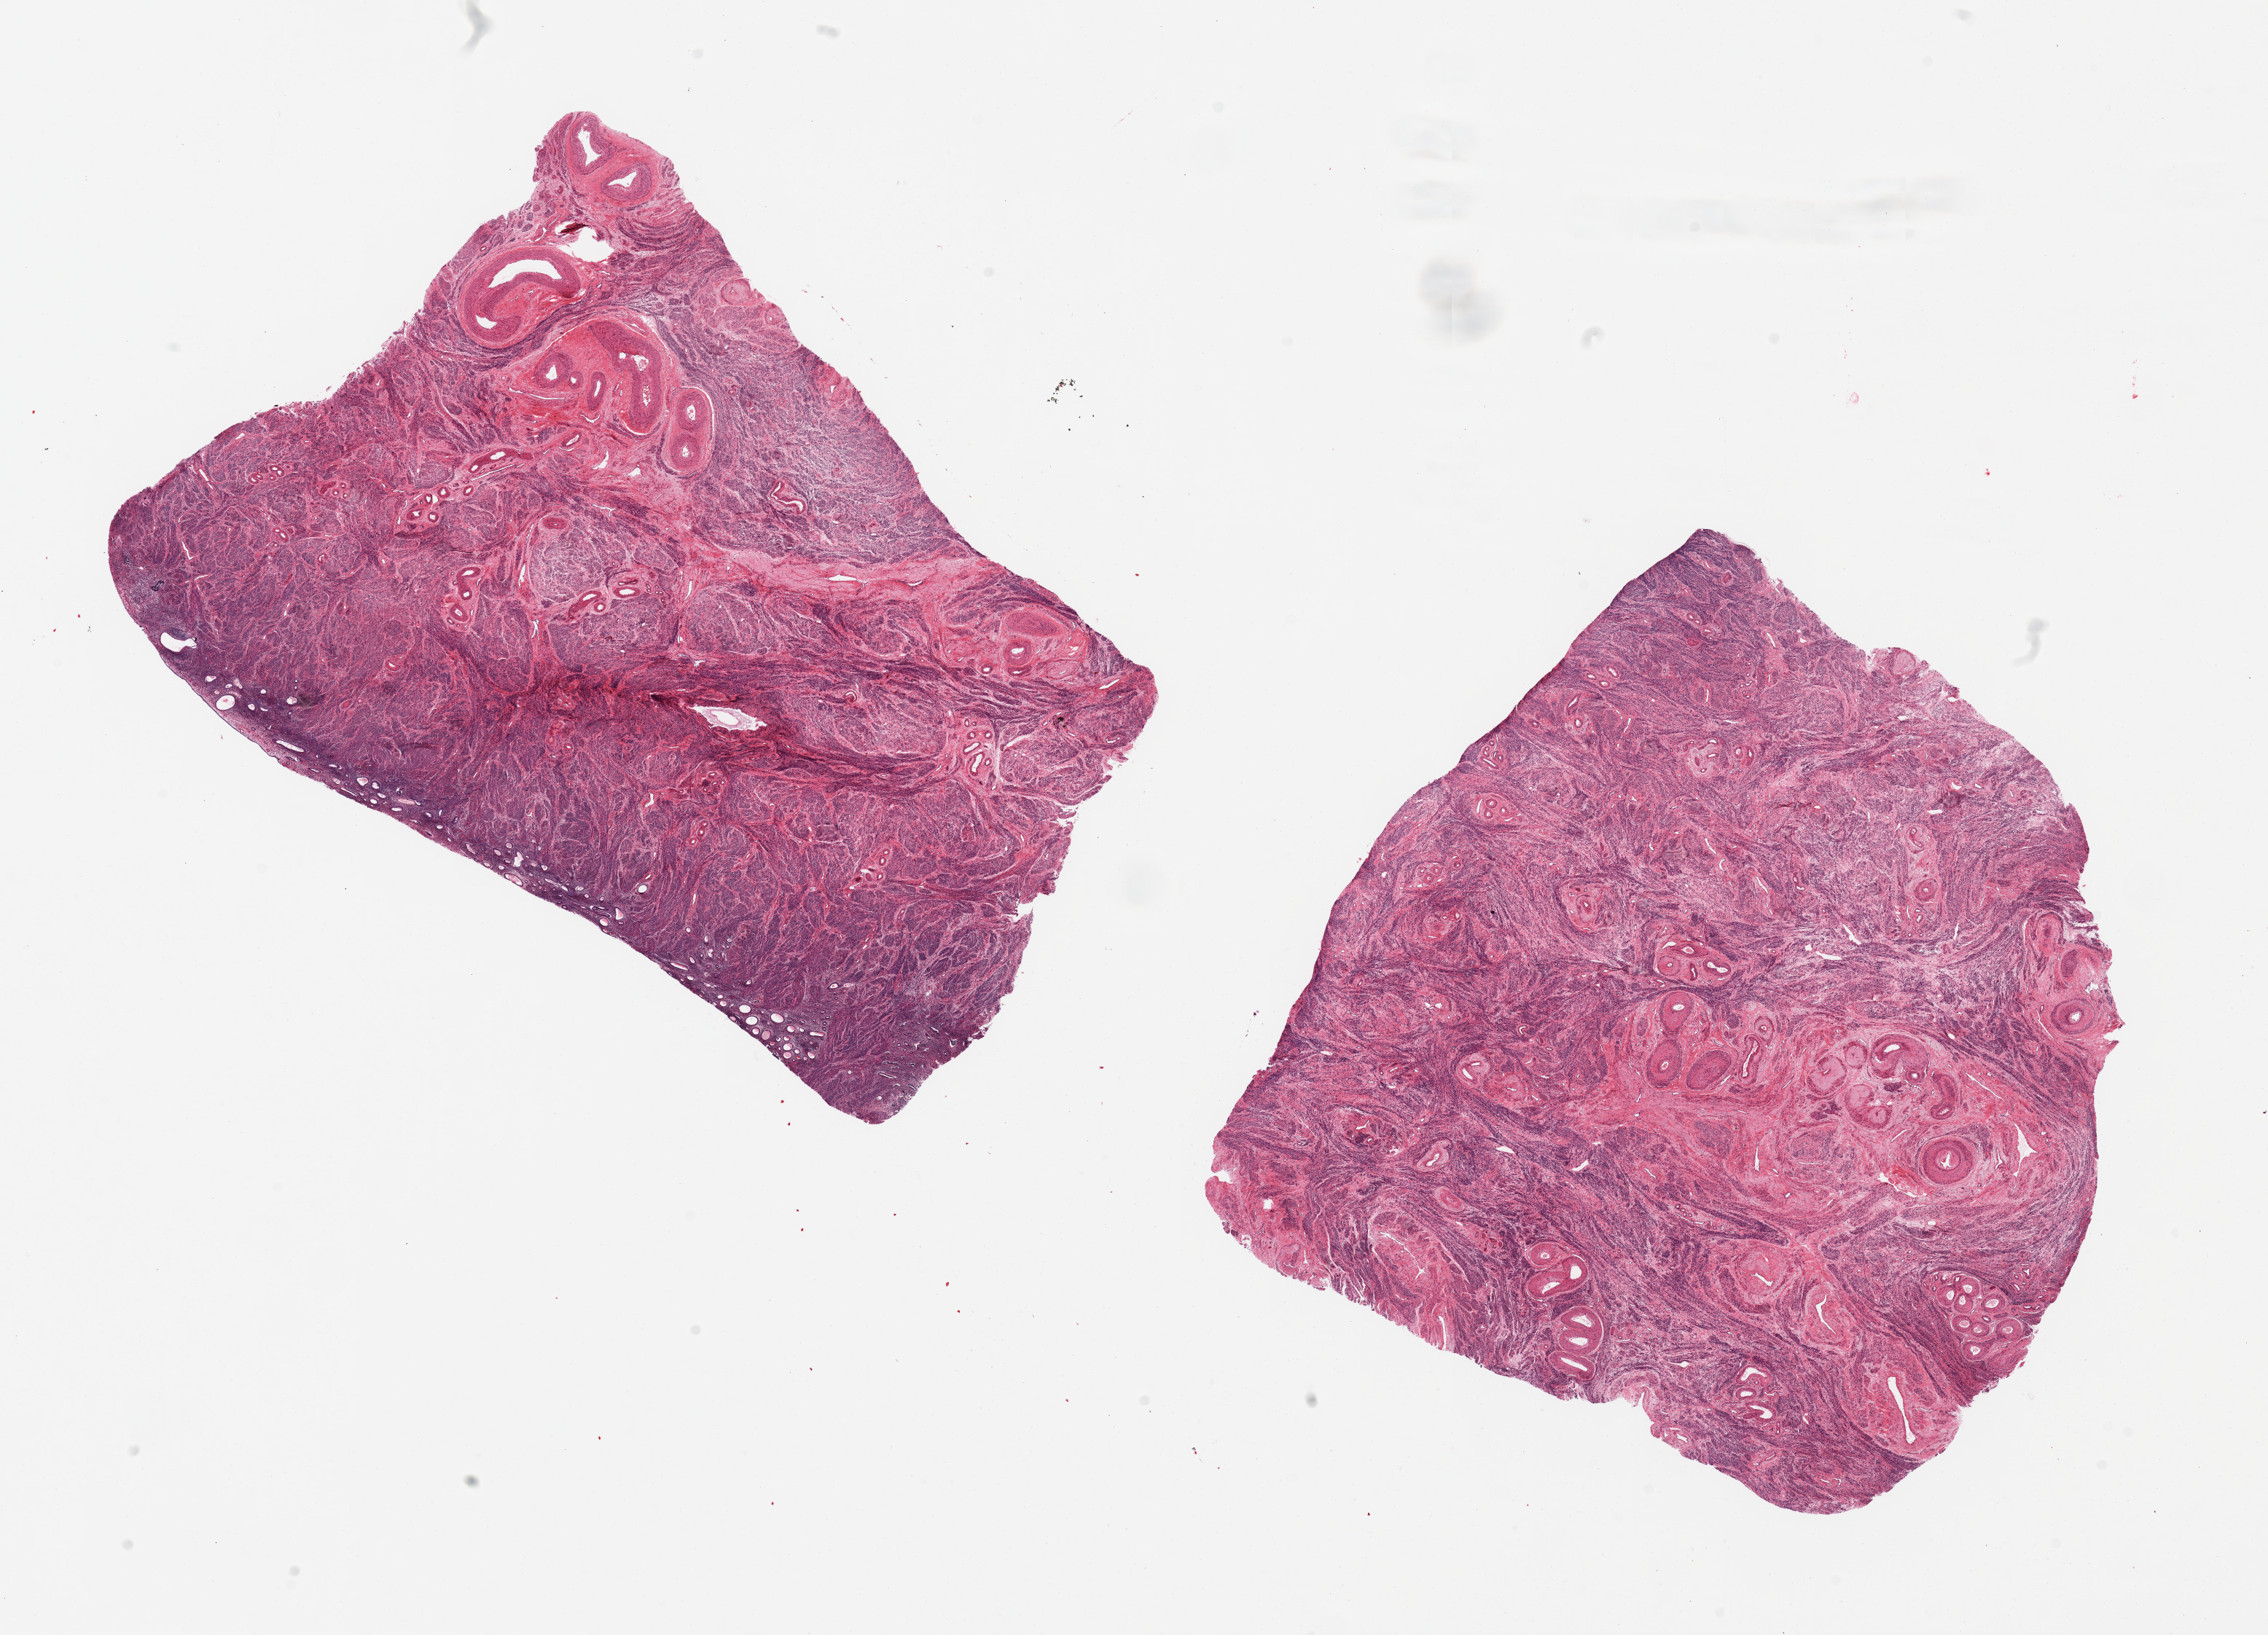
Hematoxylin and eosin (H&E) whole-slide image, brightfield — a low-resolution overview of the entire scanned area, about 24.6 x 17.7 mm (acquisition: 20x scan). PAXgene-fixed, paraffin-embedded tissue. Sampled site (target tissue): uterus. Tissue donor sample. Donor sex: female.
Pathologist's review note for this sample: 2 pieces; thin atrophic endometrium on 1 piece; no endometrium in this cut on other piece.